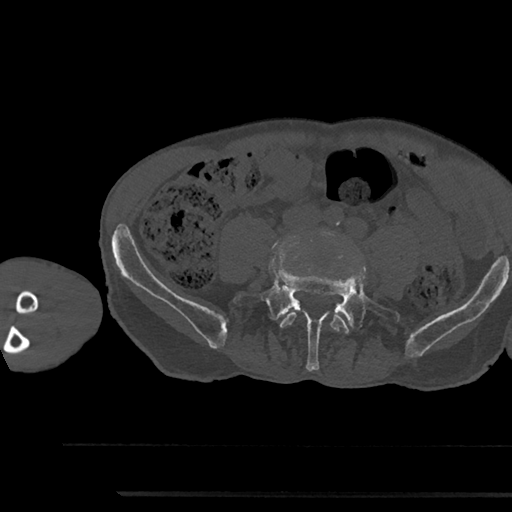
CT including the spine, one axial slice. Slice 368 of 797 in the series (ordered by position). Reconstruction kernel Br40s/3. 120 kVp. Bone window (W 1800 / L 400 HU). 0.5 mm slice thickness. 512 × 512 image matrix, field of view 367 × 367 mm. Patient: male, 79 years. Case-level facts recorded for this patient, not image findings: primary cancer: prostate.
Structures marked on this image (semi-automatic segmentation, software-assisted and operator-edited):
- L4 vertebra: bounding box [x1, y1, x2, y2] px = [280, 311, 349, 334]
- L5 vertebra: [233, 263, 400, 370]